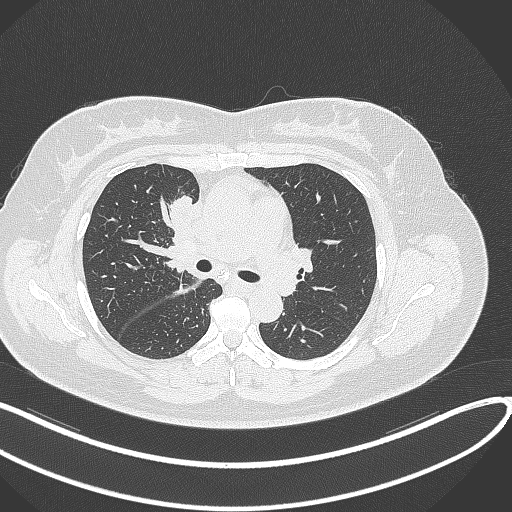
Chest CT, one axial slice. Slice 169 of 303 in the series (ordered by position). Reconstruction kernel B70f. 120 kVp. Lung window (W 1500 / L -600 HU). 1 mm slice thickness. 512 × 512 image matrix, field of view 400 × 400 mm. Female patient, age 46 years. Case-level facts recorded for this patient, not image findings: clinical TNM (as recorded): T2a N1 M0.
Outlined on this slice (bounding box drawn by a radiologist):
- lung tumour (recorded histology: adenocarcinoma): bounding box [x1, y1, x2, y2] px = [160, 190, 201, 238]